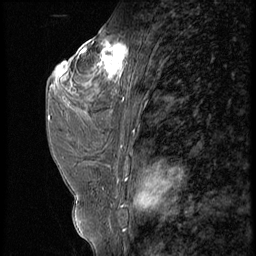
Breast MRI (dynamic contrast-enhanced), one sagittal slice. Slice 32 of 56 in the series (ordered by position). 4 images stored at this slice position (order not interpretable as contrast timing). 1.5 T. TE 4.2 ms, TR 9 ms. 256 × 256 image matrix. Patient: female, 44 years. Case-level facts recorded for this patient, not image findings: setting: breast cancer imaged before/during neoadjuvant chemotherapy; receptor status: triple-negative.
Structures marked on this image (semi-automatic segmentation, software-assisted and operator-edited):
- analysis volume of interest (the breast-tissue region the enhancement analysis was run in; not a lesion): bounding box (x1, y1, x2, y2) in pixels: (87, 28, 132, 99)
- tumour enhancement mask (voxels above the 140 % enhancement threshold inside the analysis volume of interest): (95, 42, 129, 83)